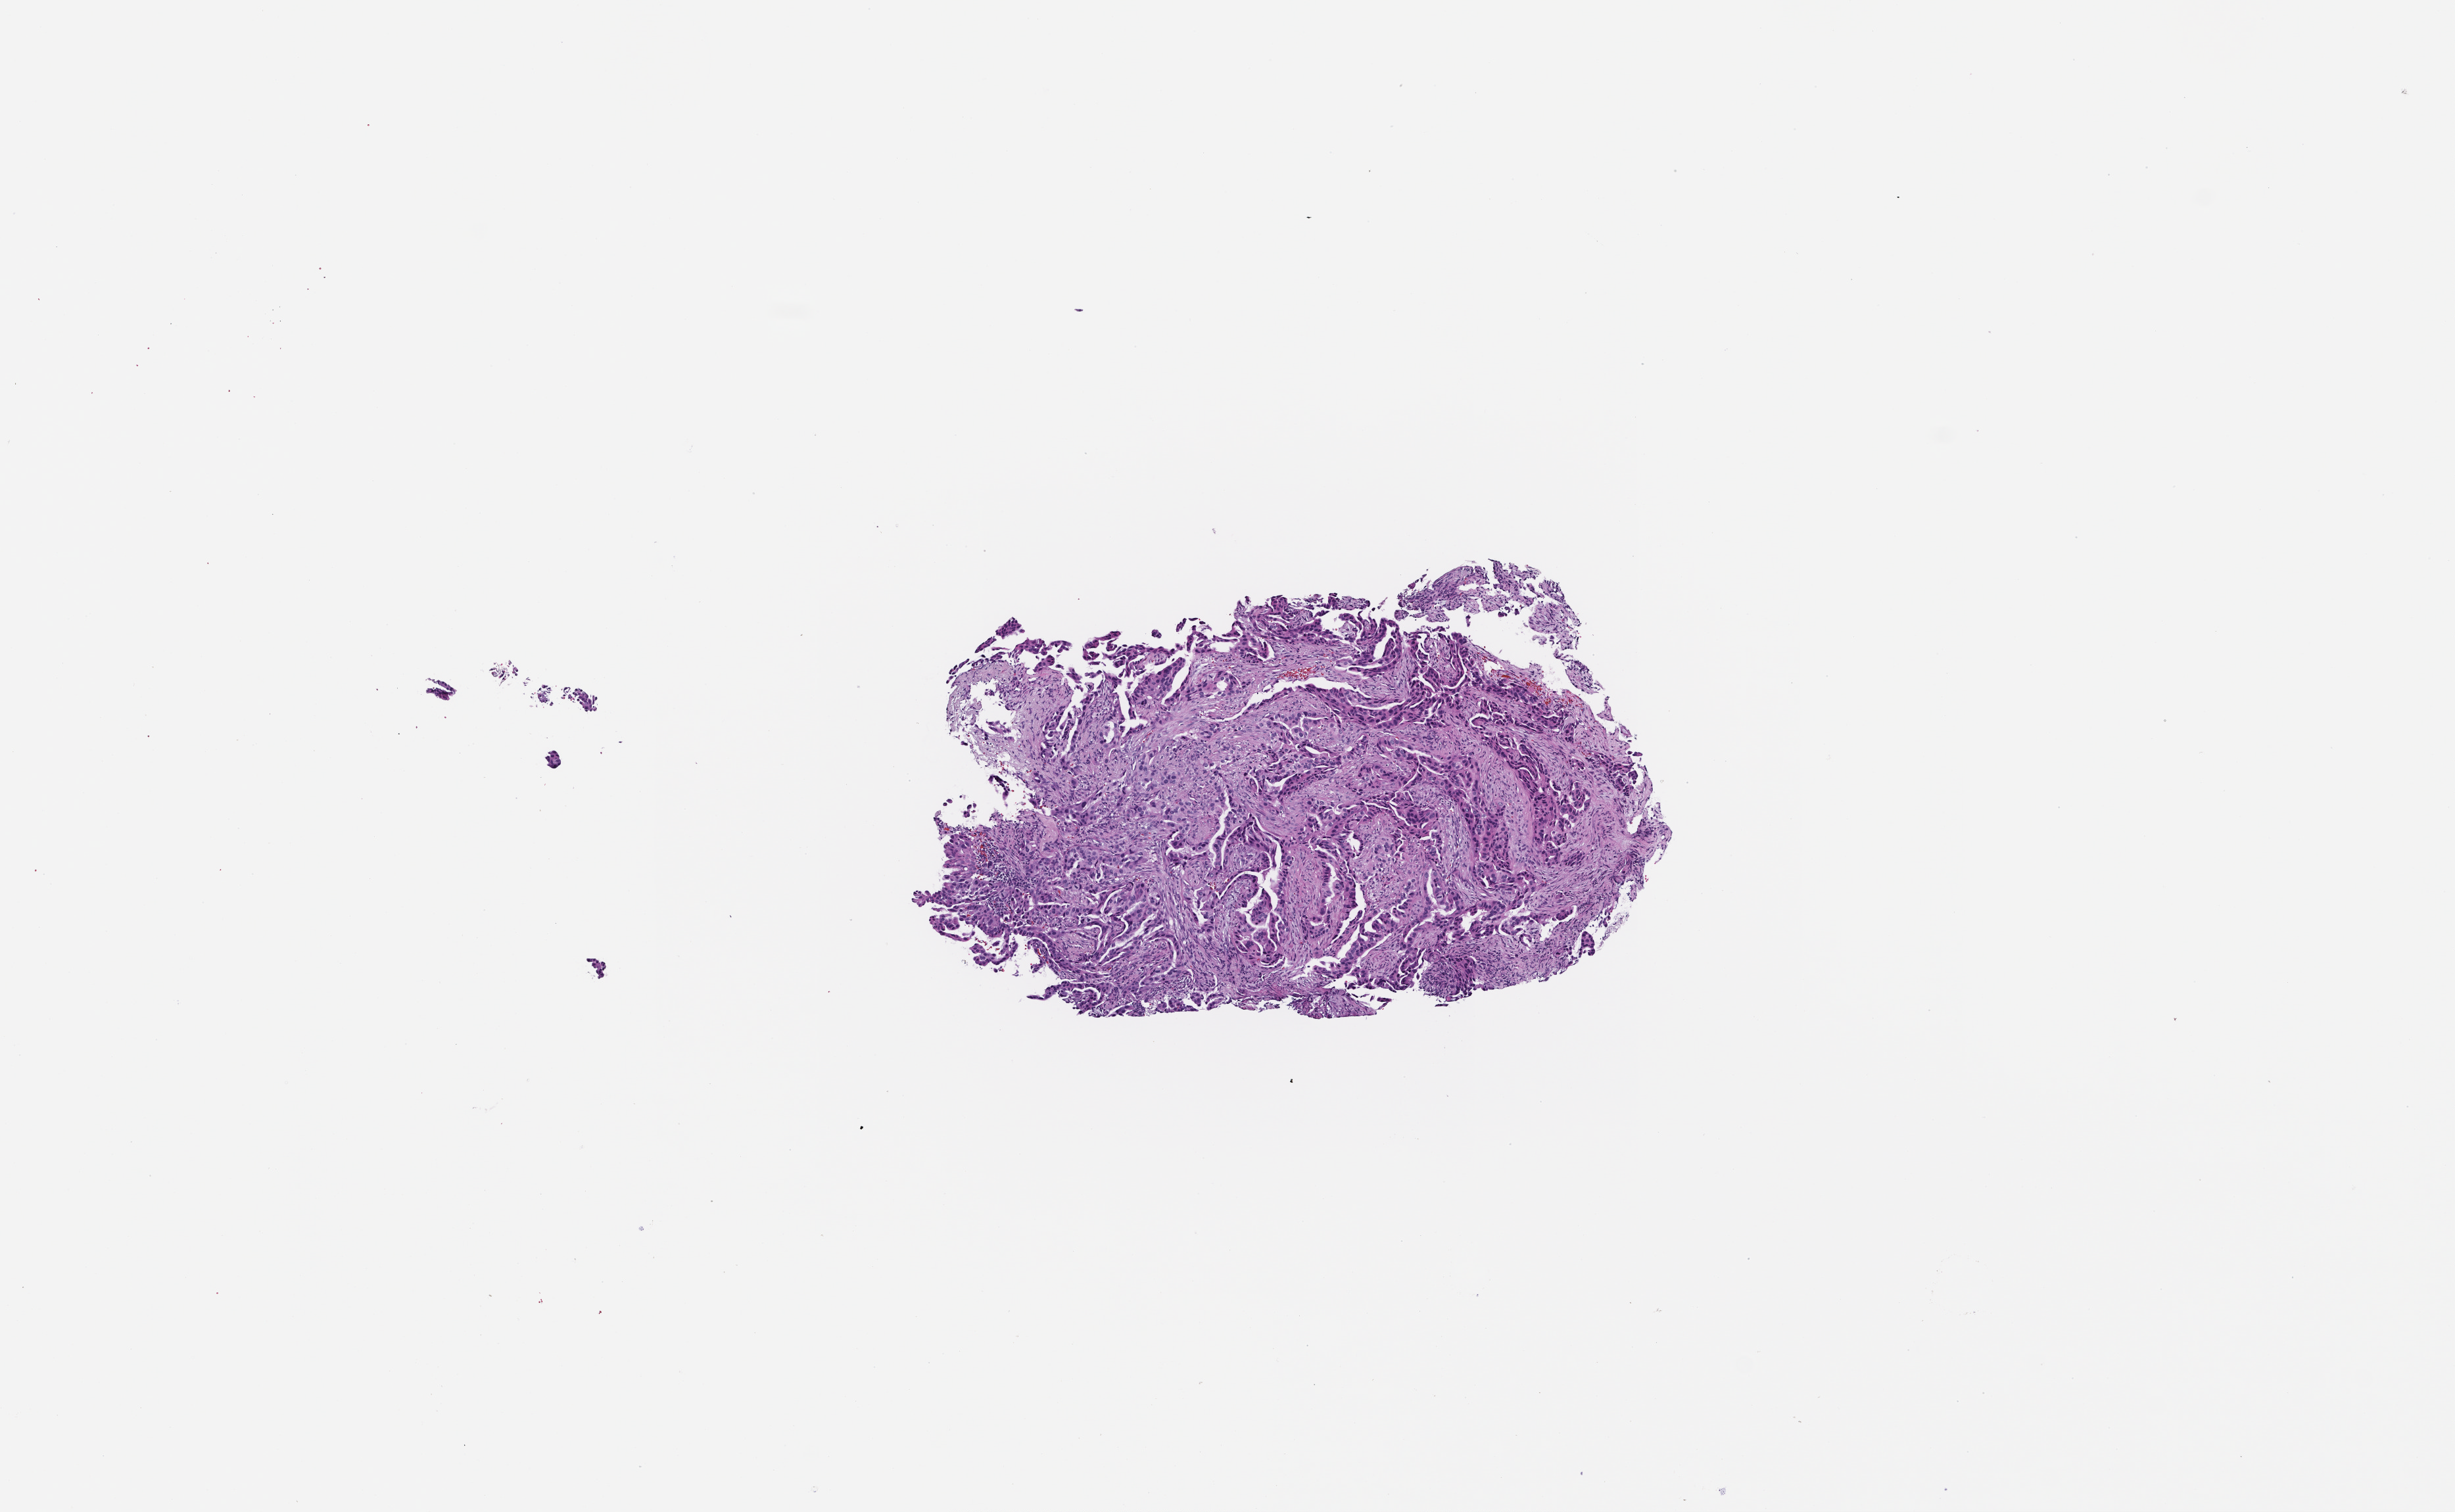
Whole-slide image, hematoxylin and eosin (H&E) stain, shown as a low-resolution overview of the whole scanned area (about 7.5 x 4.6 mm). FFPE section. Site: lung. Patient: male.
This section: primary tumor. Diagnosis: Non-Small Cell Lung Carcinoma.